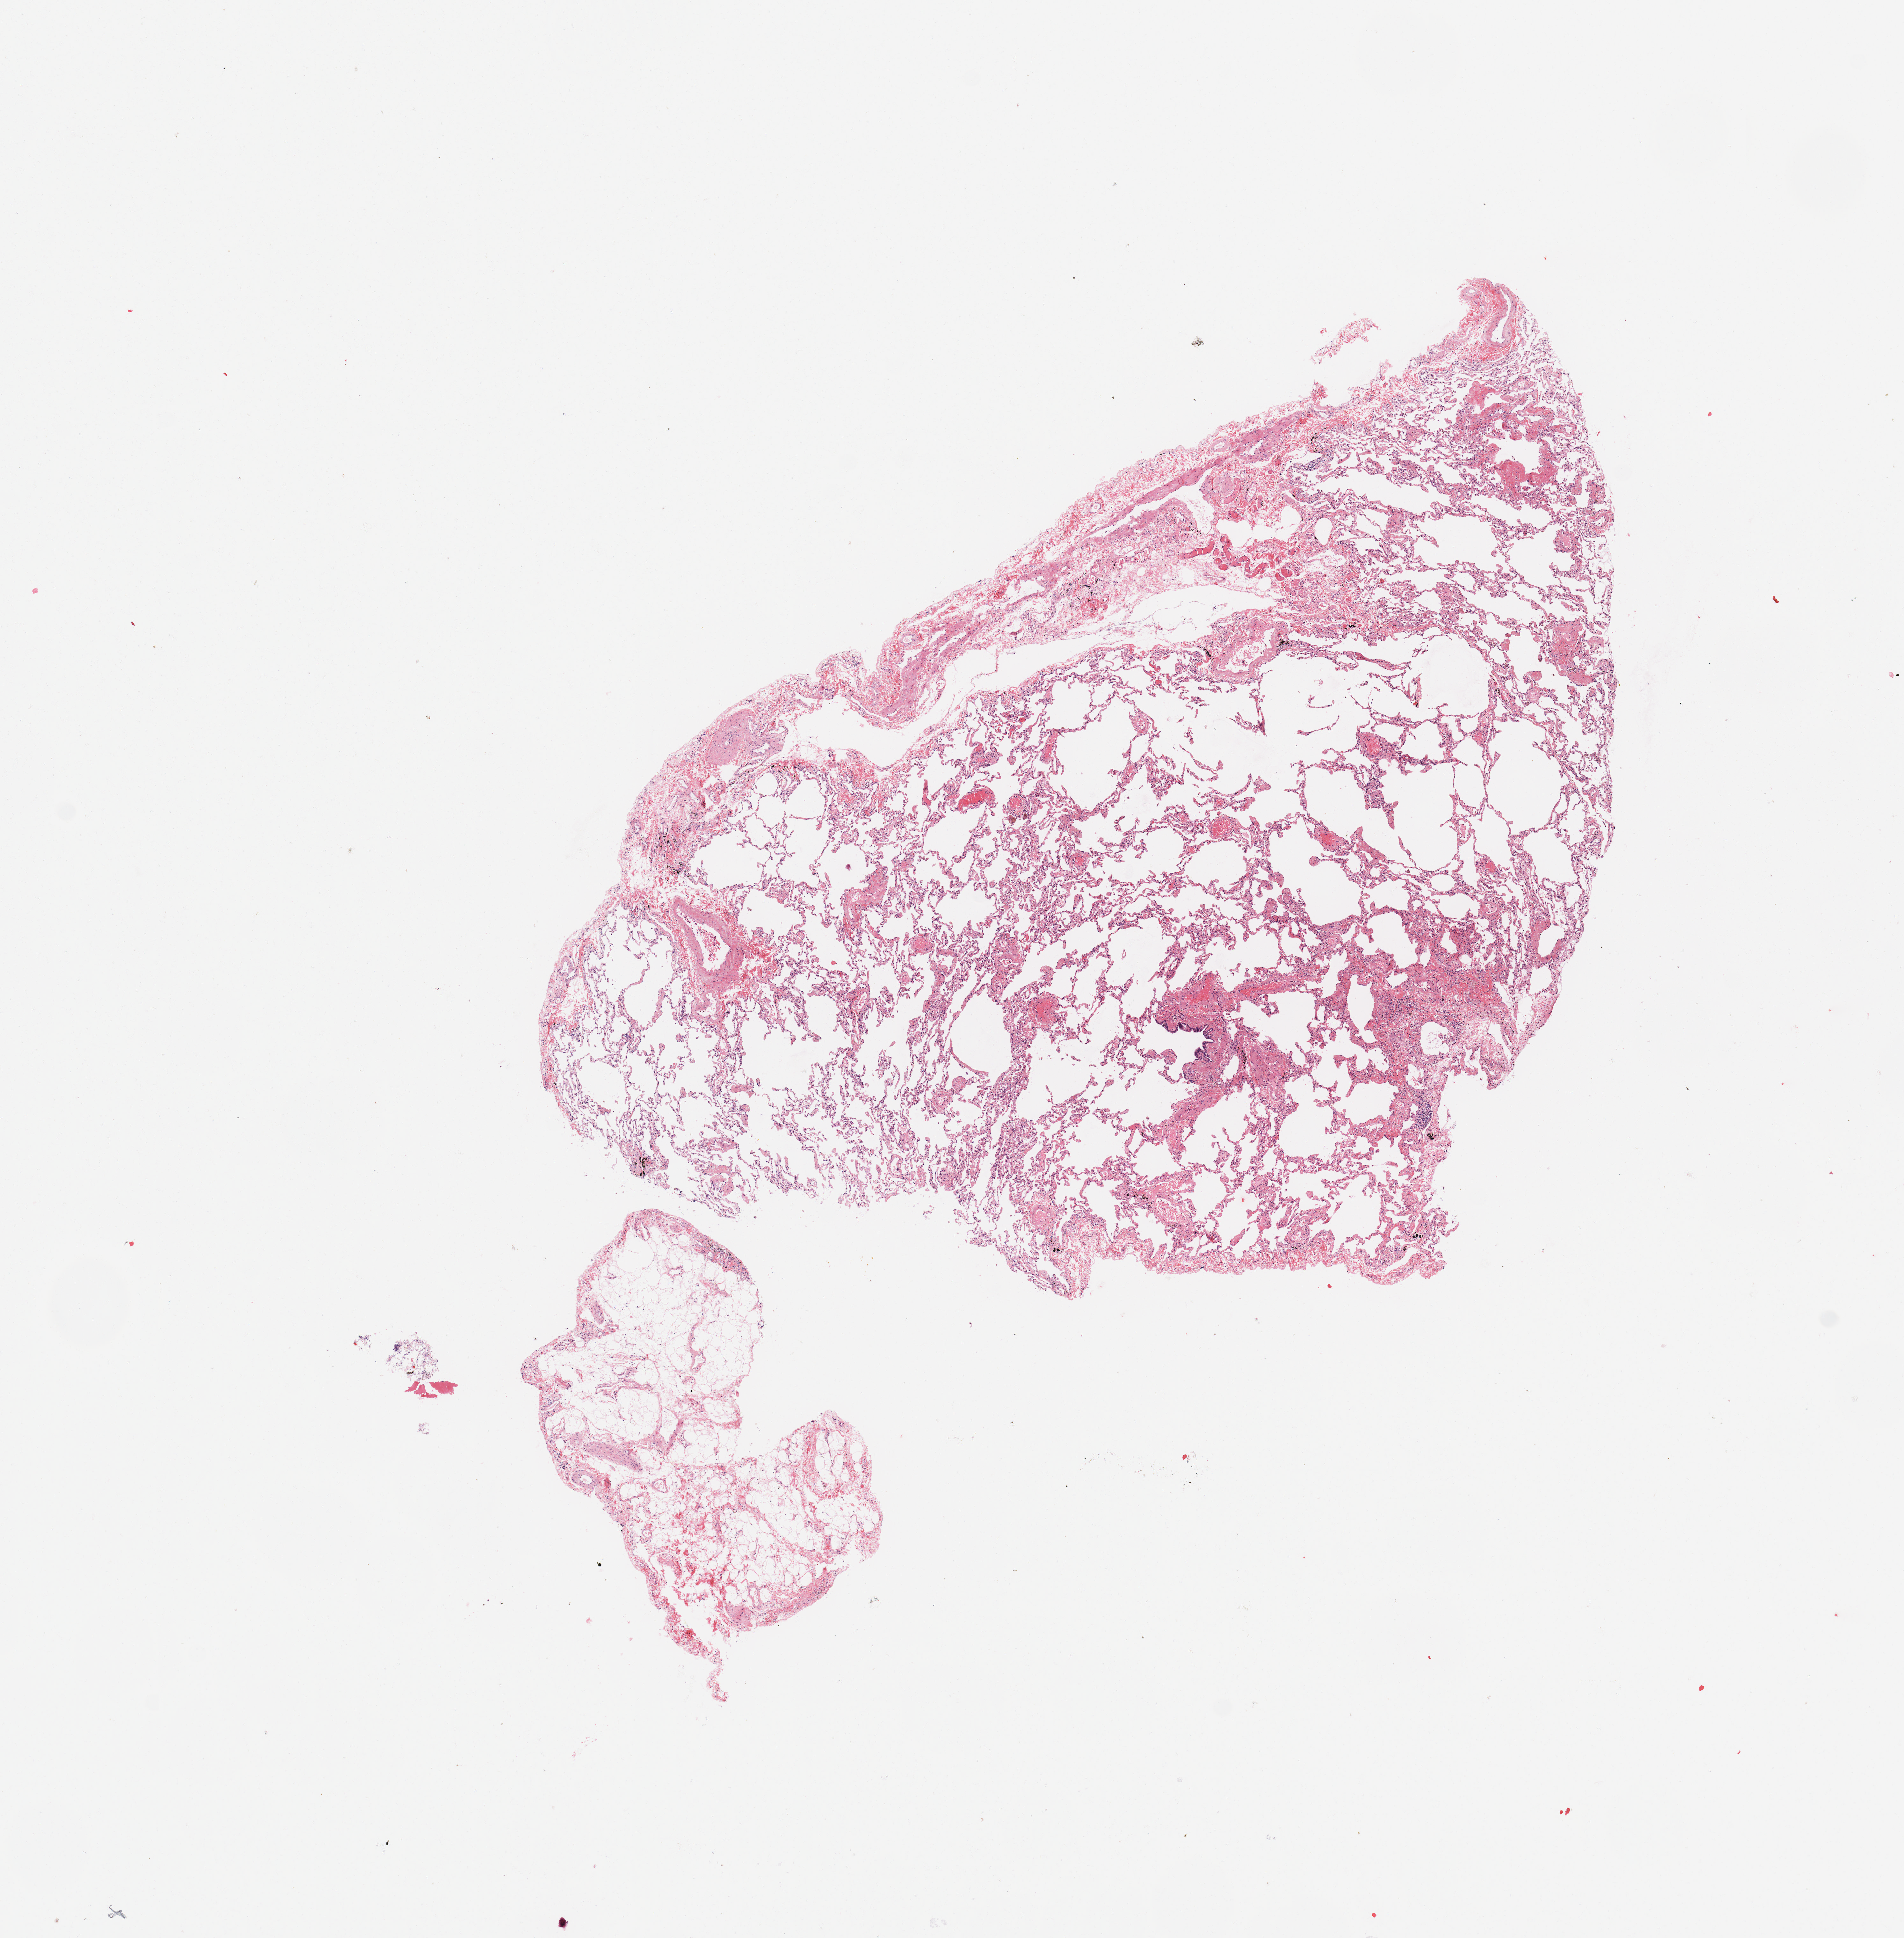
Digitized H&E tissue section (whole slide) — low-resolution overview of the scanned area, about 11.8 x 12.0 mm. Normal (non-tumour) tissue sample, sampled site: lung. Male, 72 y/o.
This section: normal (non-tumour) tissue from the same patient. Patient diagnosis: Adenocarcinoma, NOS.